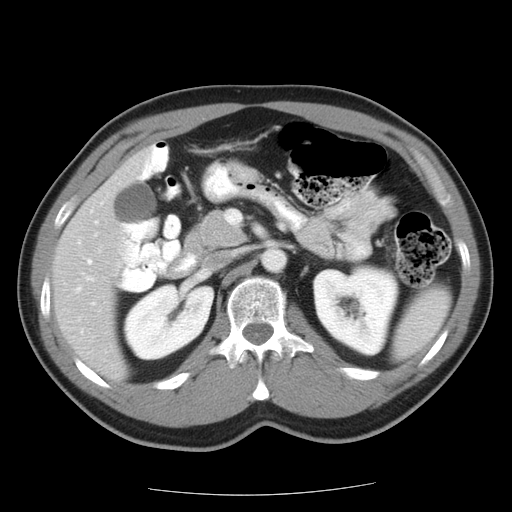
Contrast-enhanced abdominal CT, one axial slice. Position 7 of 22 along the scan axis. Reconstruction kernel STANDARD. 120 kVp. Intravenous contrast given. Soft-tissue window (W 400 / L 40 HU). 7.5 mm slice thickness. 512 × 512 image matrix, field of view 359 × 359 mm. Male patient, age 41 years. From the clinical record (not read from this slice): diagnosis: colorectal cancer liver metastases, imaged before liver resection; multiple liver metastases: no; largest metastasis: 2.7 cm; disease in both lobes: no.
Outlined on this slice (outlined manually by an expert reader):
- hepatic veins: box from (x=78, y=261) to (x=95, y=305) px
- liver: (x=55, y=158)–(x=141, y=373)
- planned liver remnant (the part of the liver to remain after resection): (x=55, y=157)–(x=142, y=373)
- portal vein (with intrahepatic branches): (x=96, y=234)–(x=98, y=236)